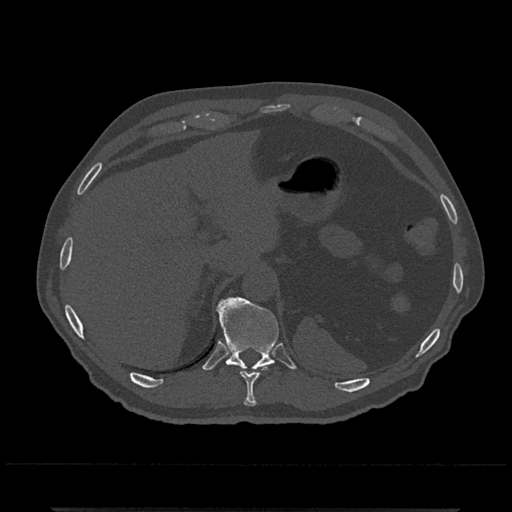
CT including the spine, one axial slice; position 519 of 797 along the scan axis; reconstruction kernel Br40s/3; 120 kVp; bone window (W 1800 / L 400 HU); 0.5 mm slice thickness; 512 × 512 image matrix, field of view 393 × 393 mm. Male patient, age 67 years. From the clinical record (not read from this slice): primary cancer: prostate.
Annotated regions visible in this slice (semi-automatic segmentation, software-assisted and operator-edited):
- T10 vertebra: bounding box (x1, y1, x2, y2) in pixels: (240, 368, 266, 407)
- T11 vertebra: (217, 297, 279, 370)